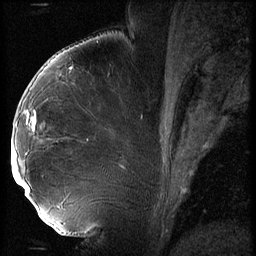
Breast MRI (dynamic contrast-enhanced), one sagittal slice; position 32 of 56 along the scan axis; 3 images stored at this slice position (order not interpretable as contrast timing); 1.5 T; TE 4.2 ms, TR 9 ms; 2.5 mm slice thickness; 256 × 256 image matrix. Patient: female, 43 years. From the clinical record (not read from this slice): setting: breast cancer imaged before/during neoadjuvant chemotherapy; receptor status: HER2-positive.
Annotated regions visible in this slice (semi-automatic segmentation, software-assisted and operator-edited):
- analysis volume of interest (the breast-tissue region the enhancement analysis was run in; not a lesion): bounding box [x1, y1, x2, y2] px = [12, 92, 74, 211]
- tumour enhancement mask (voxels above the 140 % enhancement threshold inside the analysis volume of interest): [12, 121, 29, 197]